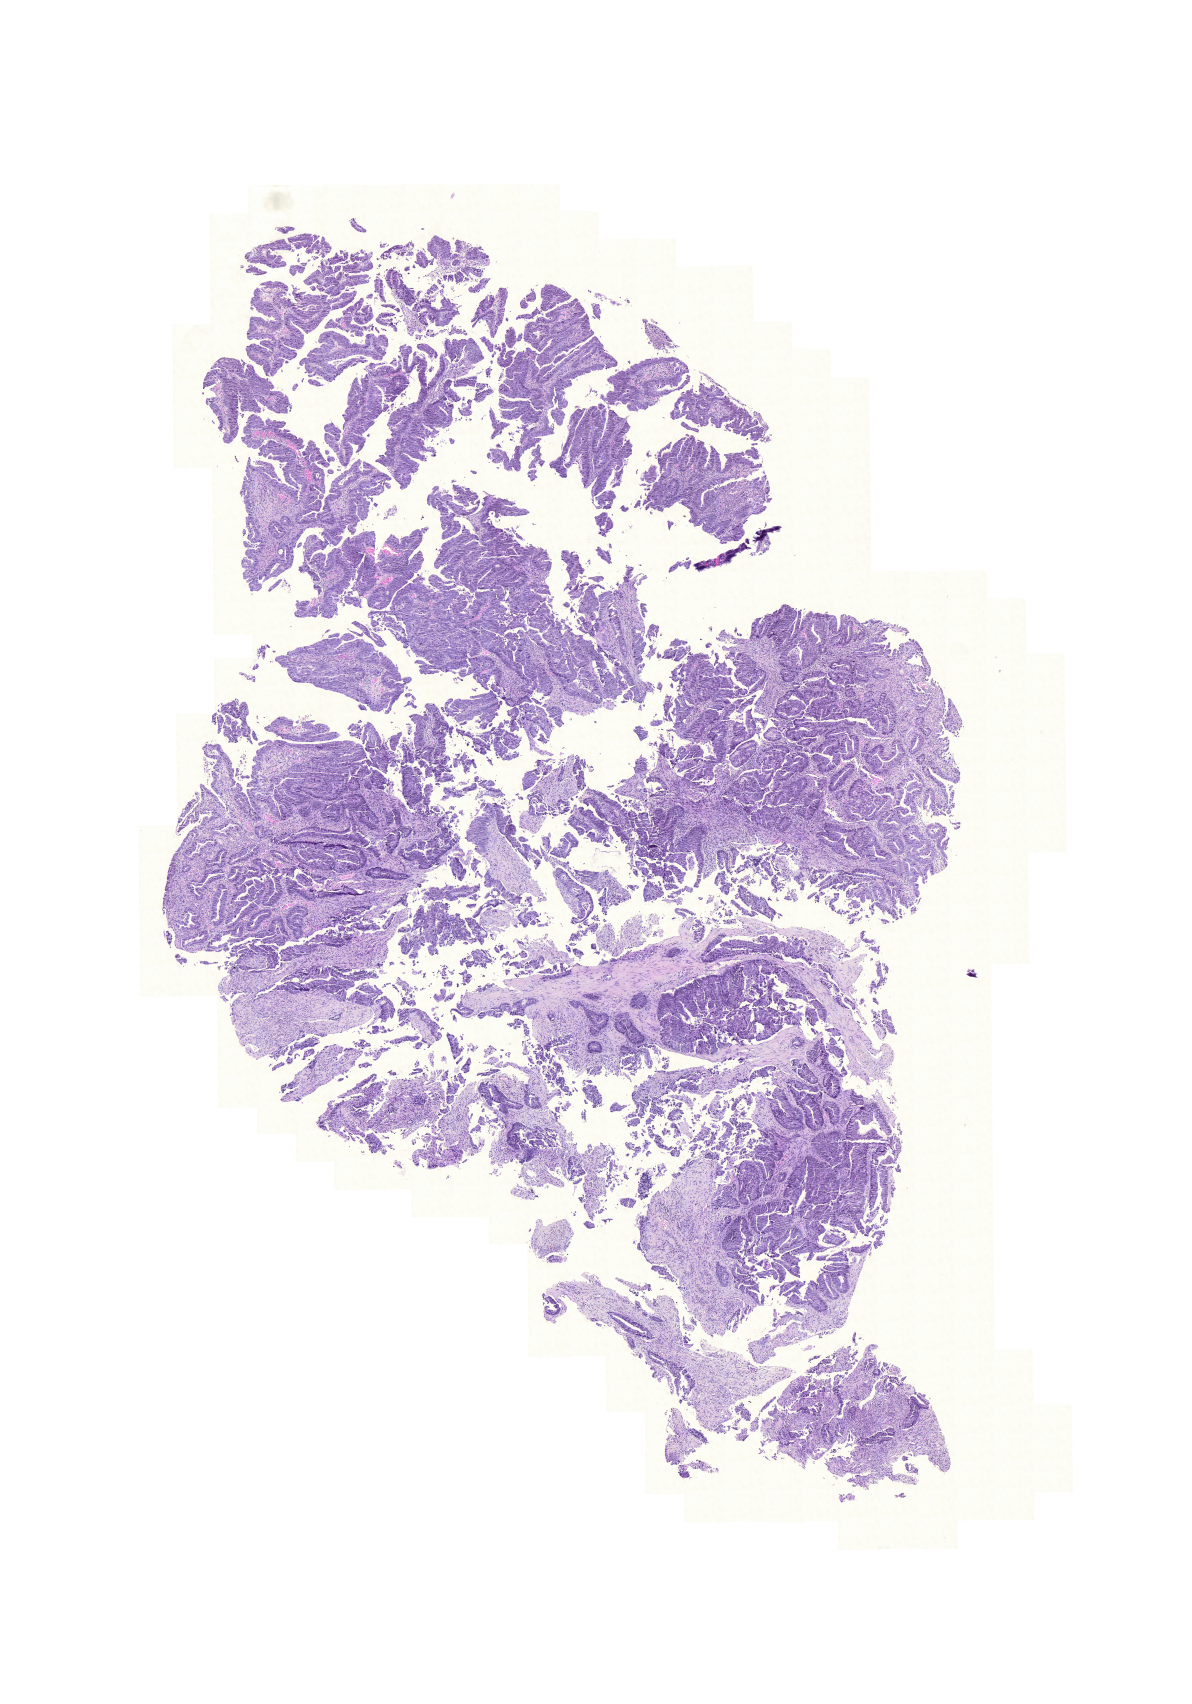
Whole-slide histology image, H&E — low-resolution overview of the scanned area, about 8.9 x 12.7 mm; FFPE section; primary tumour sample from the colon. Female, age 73 years at initial diagnosis.
AJCC pathologic stage: I. Pathologic diagnosis: Adenocarcinoma, NOS (sigmoid colon).